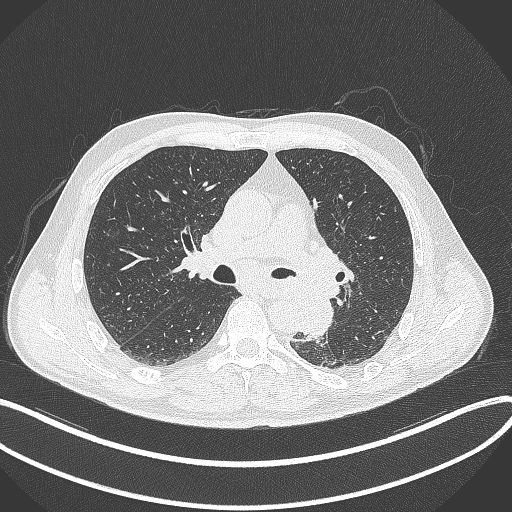
Chest CT, one axial slice. Slice 204 of 329 in the series (ordered by position). Reconstruction kernel B70f. 120 kVp. Lung window (W 1500 / L -600 HU). 512 × 512 image matrix. Patient: male, 59 years. From the clinical record (not read from this slice): clinical TNM (as recorded): T2a N2 M0.
Structures marked on this image (bounding box drawn by a radiologist):
- lung tumour (recorded histology: squamous cell carcinoma): bounding box (x1, y1, x2, y2) in pixels: (292, 290, 336, 340)